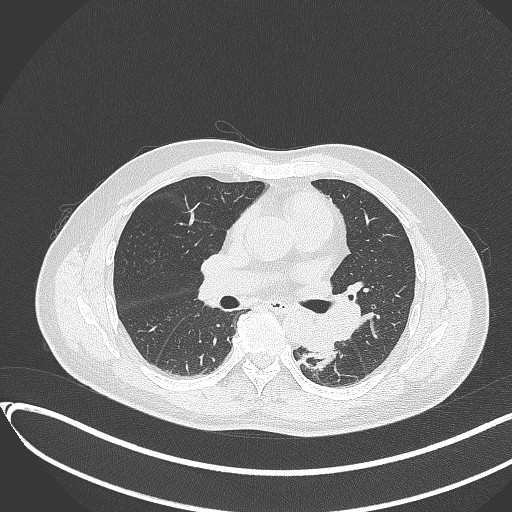
Chest CT, one axial slice. Slice 188 of 417 in the series (ordered by position). 120 kVp. Lung window (W 1500 / L -600 HU). 1 mm slice thickness. 512 × 512 image matrix, field of view 400 × 400 mm. Male patient, age 54 years. Case-level facts recorded for this patient, not image findings: clinical TNM (as recorded): T3 N0 M0.
Outlined on this slice (rectangle marked by the reading radiologist):
- lung tumour (recorded histology: squamous cell carcinoma): bounding box <302,316,339,366> (left, top, right, bottom; pixels)